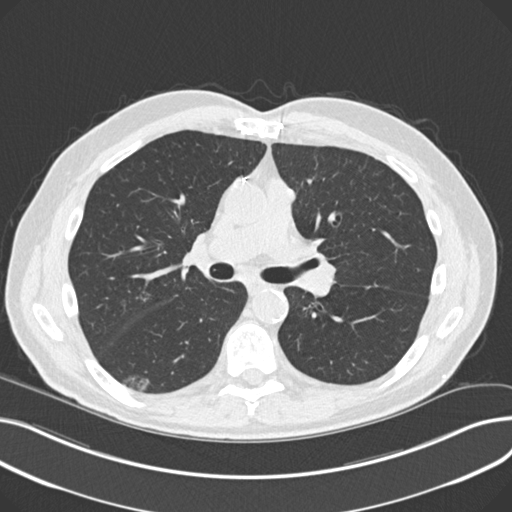
Low-dose screening chest CT, one axial slice; slice 128 of 230 in the series (ordered by position); reconstruction kernel B30f; 120 kVp; lung window (W 1500 / L -600 HU); 2 mm slice thickness; 512 × 512 image matrix.
Structures marked on this image (manually delineated by an expert):
- lesion 1 (nodule, lower lobe of right lung): bounding box (x1, y1, x2, y2) in pixels: (123, 376, 150, 391)